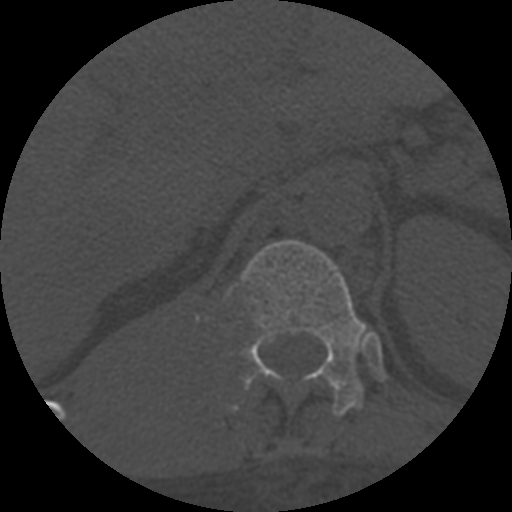
CT including the spine, one axial slice; slice 318 of 708 in the series (ordered by position); reconstruction kernel STANDARD; one of 3 acquisitions stored at this slice position; bone window (W 1800 / L 400 HU); 512 × 512 image matrix. Patient age 55 years. From the clinical record (not read from this slice): primary cancer: colon; vertebrae with lytic lesions (as recorded): T12, L1, L5.
Outlined on this slice (semi-automatic segmentation, software-assisted and operator-edited):
- T11 vertebra: box from (x=232, y=408) to (x=237, y=409) px
- T12 vertebra: (x=225, y=240)–(x=367, y=417)